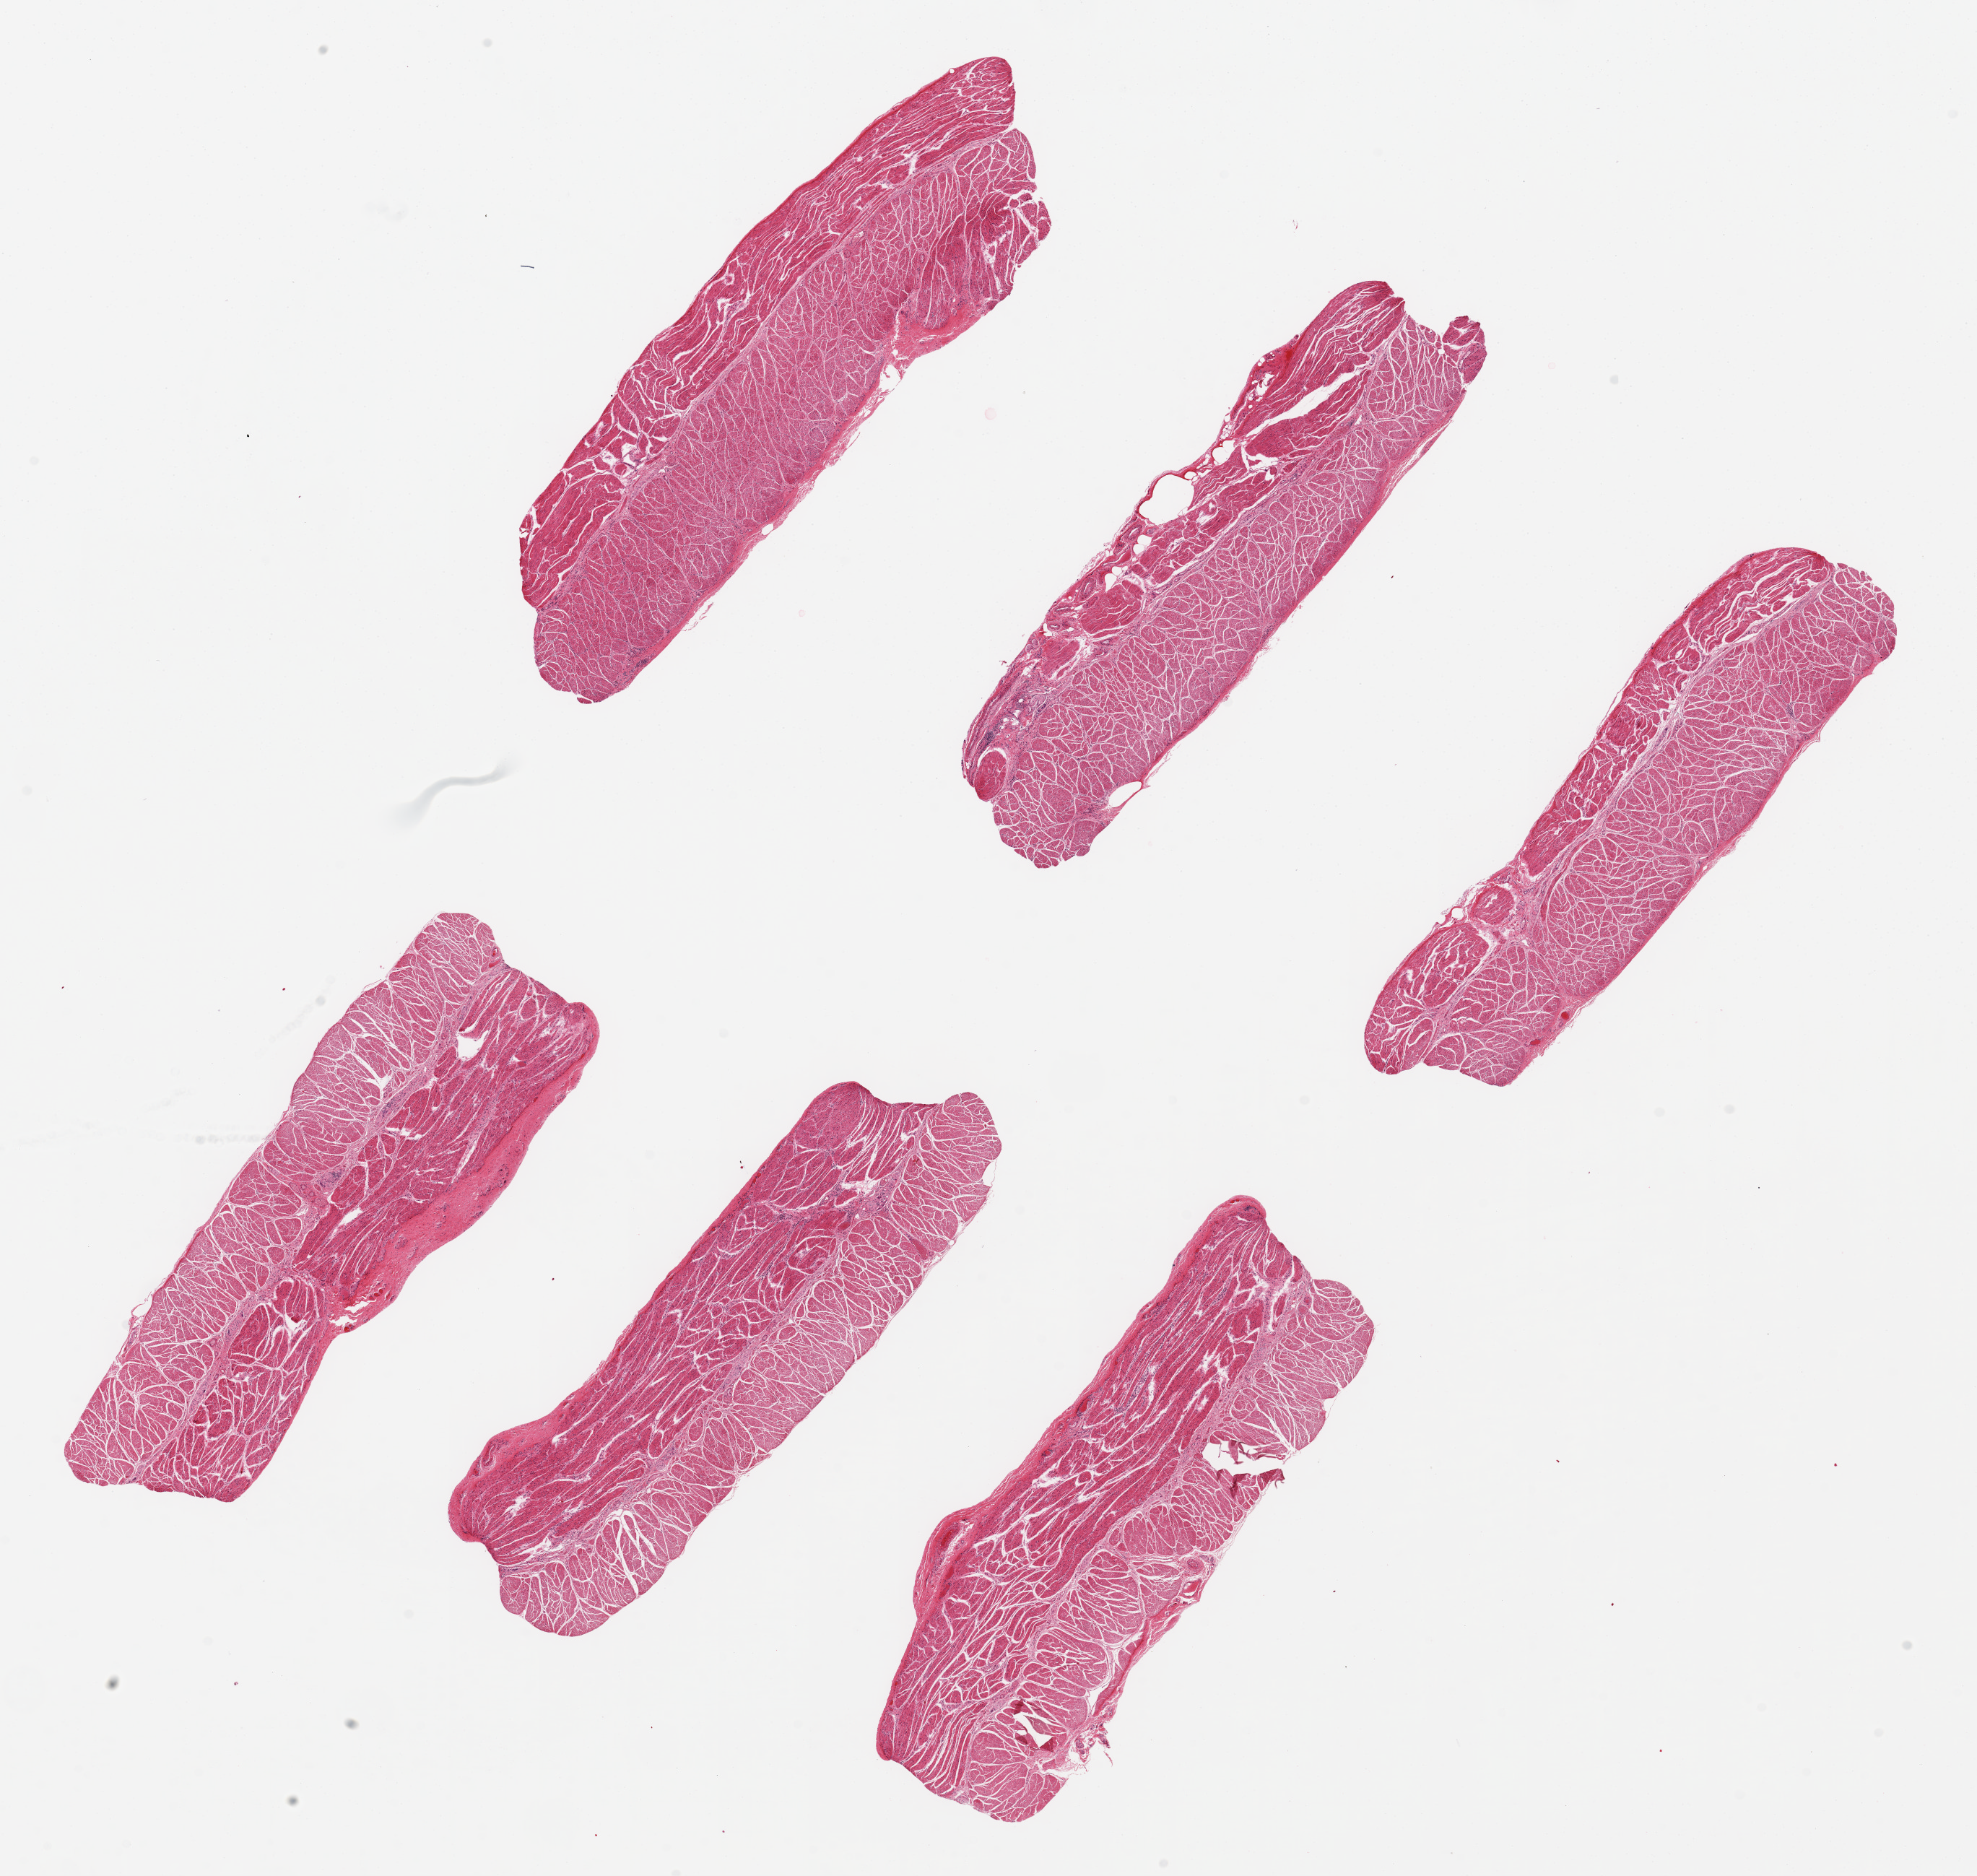
Digitized haematoxylin and eosin-stained section, a low-resolution overview of the entire scanned area, about 21.7 x 20.5 mm. PAXgene-fixed paraffin-embedded (PFPE) section. Section of esophageal muscle (target tissue). Tissue donor sample. Male donor.
Reviewer comment on this tissue sample: 6 ~7x2mm pieces.